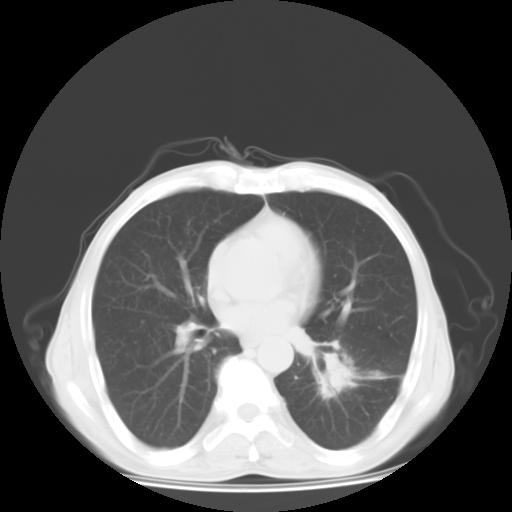
Chest CT, one axial slice; position 10 of 27 along the scan axis; reconstruction kernel STANDARD; lung window (W 1500 / L -600 HU); 10 mm slice thickness; 512 × 512 image matrix, field of view 350 × 350 mm. Patient: male, 63 years. Case-level facts recorded for this patient, not image findings: clinical TNM (as recorded): T1c N0 M1b.
Annotated regions visible in this slice (bounding box drawn by a radiologist):
- lung tumour (recorded histology: adenocarcinoma): bounding box (x1, y1, x2, y2) in pixels: (306, 340, 376, 404)